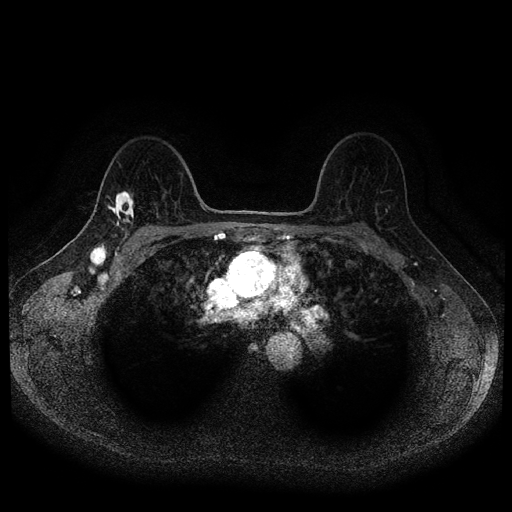
Breast MRI (dynamic contrast-enhanced, multi-phase), one axial slice; position 71 of 116 along the scan axis; dynamic contrast-enhanced series, time point 2 of 5 at this slice position (early post-contrast); 1.5 T; TE 2.6 ms, TR 5.4 ms; 2 mm slice thickness; 512 × 512 image matrix, field of view 340 × 340 mm. Female patient, age 49 years.
Structures marked on this image (semi-automatically segmented with operator editing):
- breast lesion (labelled 'tumour' in the annotation; benign lesions carry a separate 'benign' label): bounding box <105,188,139,229> (left, top, right, bottom; pixels)